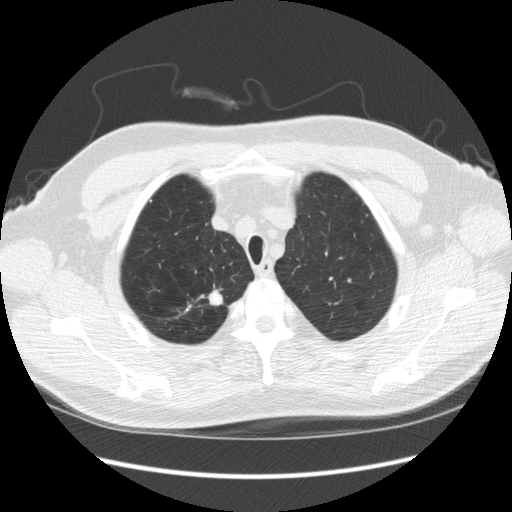
Chest CT (low-dose screening protocol), one axial image; third screening round (two years after baseline); lung window (W 1500 / L -600 HU); 512 × 512 image matrix, field of view 380 × 380 mm. Male, age 64 years at enrolment.
• Expert reader's lesion annotation, bounding box <194,282,230,315> (left, top, right, bottom; pixels).
• The screening reader recorded 4 non-calcified nodules or masses ≥4 mm on this exam (right upper lobe, right upper lobe, right upper lobe, right upper lobe); which of them this box marks is not recorded.
• Lung cancer was diagnosed 15 days after this screen: adenocarcinoma, NOS, right upper lobe, moderately differentiated (G2), stage IA (AJCC 6th edition), 14 mm at pathology.